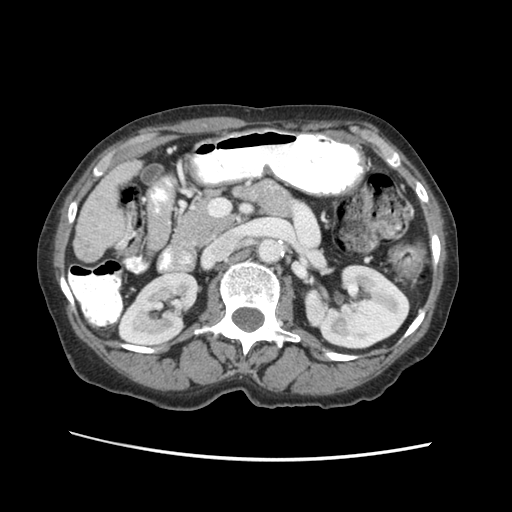
Contrast-enhanced abdominal CT (liver protocol), one axial slice; slice 13 of 63 in the series (ordered by position); soft-tissue window (W 400 / L 40 HU); 2.5 mm slice thickness; 512 × 512 image matrix, field of view 340 × 340 mm. Case-level facts recorded for this patient, not image findings: diagnosis: hepatocellular carcinoma (patient treated with transarterial chemoembolisation; whether this scan precedes or follows treatment is not stated here); TNM stage (as recorded): Stage-I; Child-Pugh class: B; tumour differentiation: well differentiated; tumour nodularity: uninodular.
Outlined on this slice (semi-automatic segmentation, software-assisted and operator-edited):
- liver parenchyma outside the tumour (the mass and vessels are separate outlines, so this box may not span the whole liver): bounding box <74,158,140,262> (left, top, right, bottom; pixels)